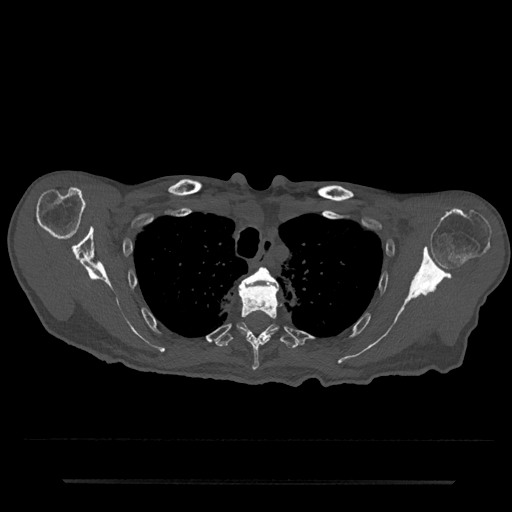
CT including the spine, one axial slice. Slice 611 of 797 in the series (ordered by position). 120 kVp. Bone window (W 1800 / L 400 HU). 0.5 mm slice thickness. 512 × 512 image matrix. Patient: male, 74 years. Case-level facts recorded for this patient, not image findings: primary cancer: prostate.
Outlined on this slice (semi-automatically segmented with operator editing):
- T3 vertebra: bounding box [x1, y1, x2, y2] px = [240, 266, 279, 290]
- T4 vertebra: [239, 284, 279, 371]
- T5 vertebra: [214, 323, 300, 349]